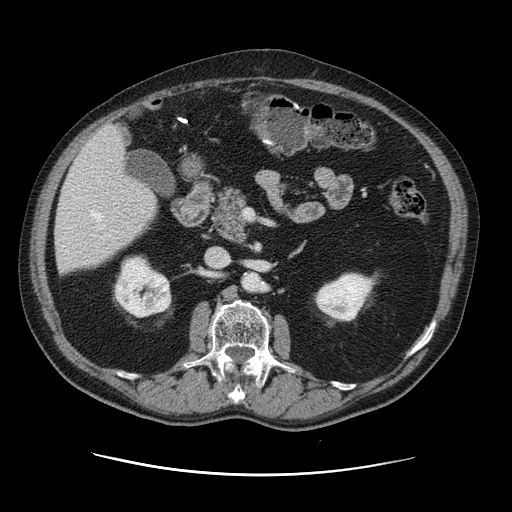
Contrast-enhanced abdominal CT, one axial slice. Slice 56 of 141 in the series (ordered by position). 120 kVp. Soft-tissue window (W 400 / L 40 HU). 512 × 512 image matrix, field of view 395 × 395 mm. Male patient, age 72 years. Case-level facts recorded for this patient, not image findings: diagnosis: colorectal cancer liver metastases, imaged before liver resection; multiple liver metastases: yes; largest metastasis: 5.4 cm; disease in both lobes: yes.
Outlined on this slice (manually delineated by an expert):
- hepatic veins: box from (x=90, y=212) to (x=105, y=229) px
- liver: (x=56, y=127)–(x=157, y=272)
- planned liver remnant (the part of the liver to remain after resection): (x=56, y=181)–(x=157, y=272)
- portal vein (with intrahepatic branches): (x=97, y=226)–(x=102, y=228)